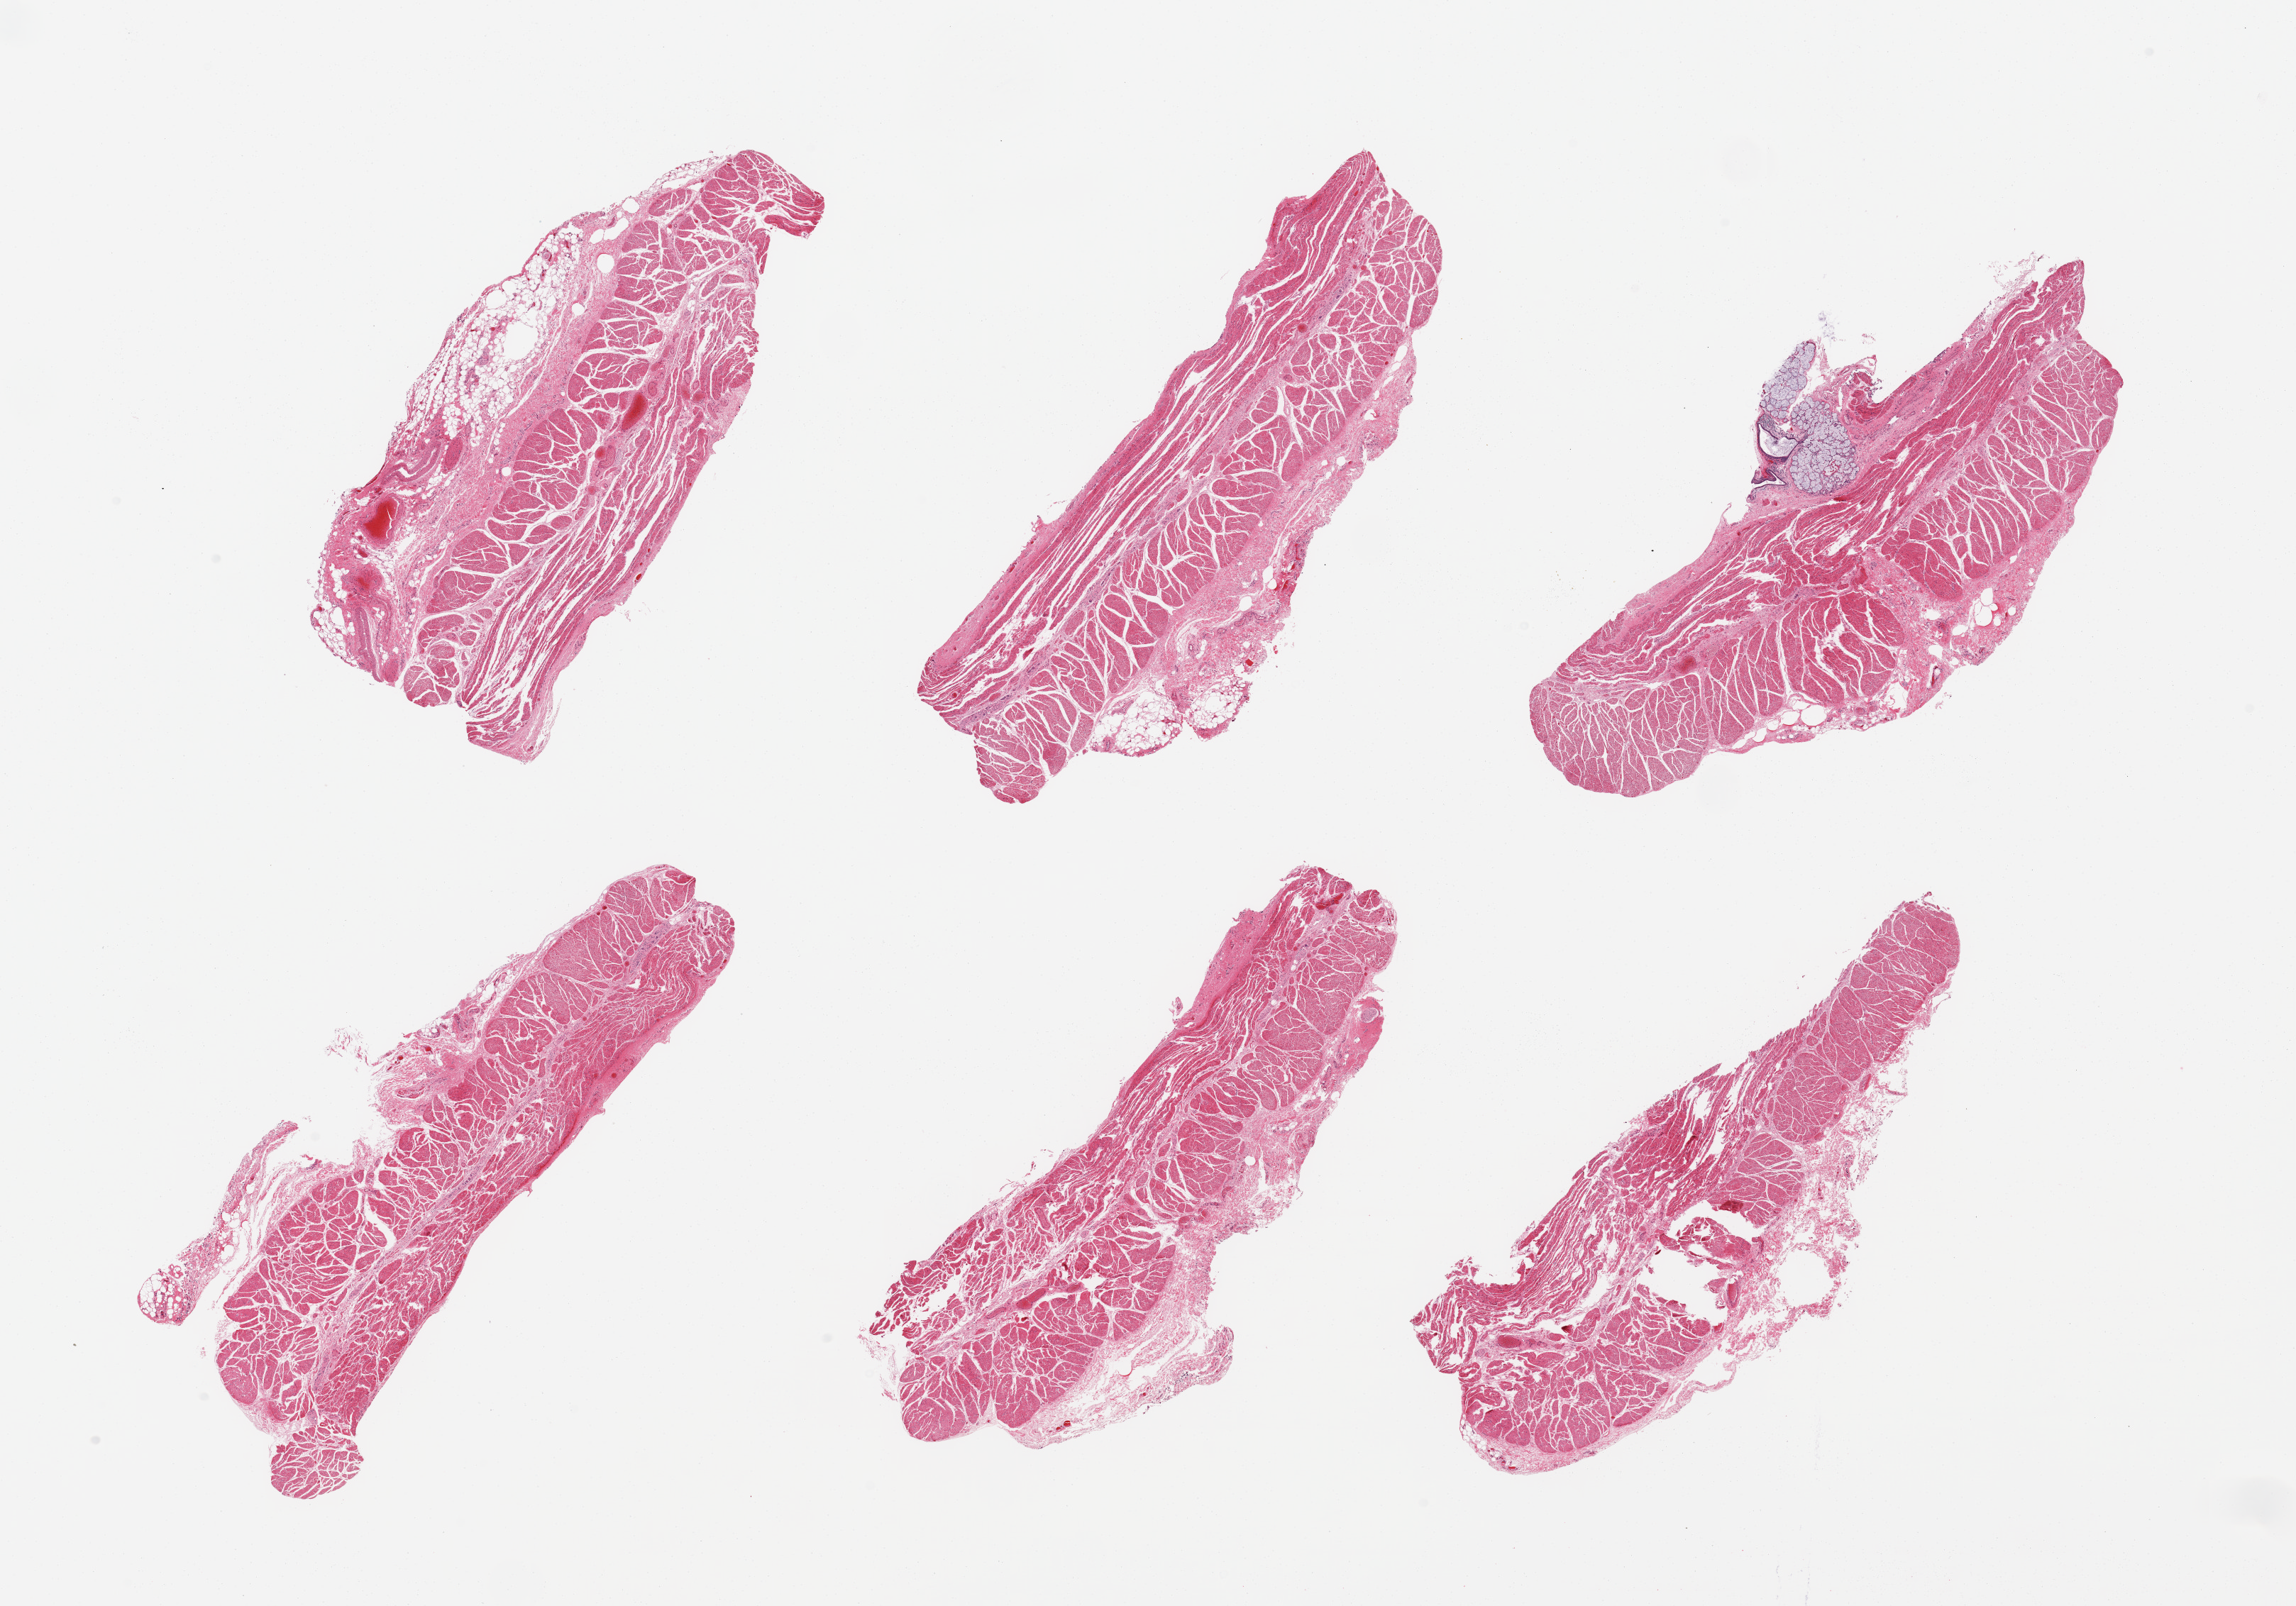
Digitized haematoxylin and eosin-stained section, brightfield, shown as a low-resolution overview of the whole scanned area (about 25.6 x 17.9 mm); PAXgene-fixed, paraffin-embedded tissue; target tissue: esophageal muscle; donor tissue sample.
• pathologist's review note for this sample: 6 pieces, confirmed target muscularis; Incidental ~1.5mm mucus gland